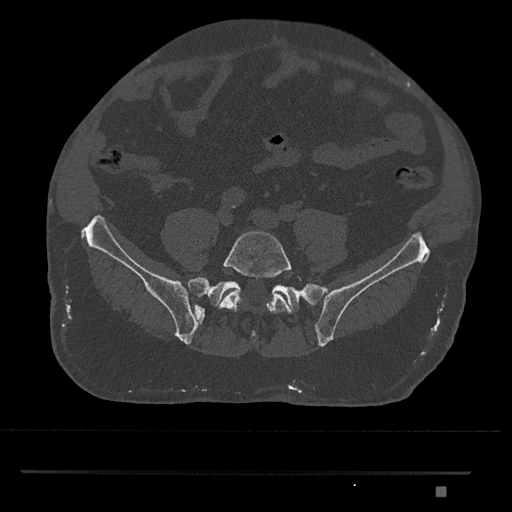
CT including the spine, one axial slice; reconstruction kernel Br40s/3; 120 kVp; bone window (W 1800 / L 400 HU); 0.5 mm slice thickness; 512 × 512 image matrix, field of view 429 × 429 mm. Patient: male, 65 years. Case-level facts recorded for this patient, not image findings: primary cancer: prostate.
Annotated regions visible in this slice (semi-automatic segmentation, software-assisted and operator-edited):
- L5 vertebra: bounding box (x1, y1, x2, y2) in pixels: (219, 230, 302, 314)